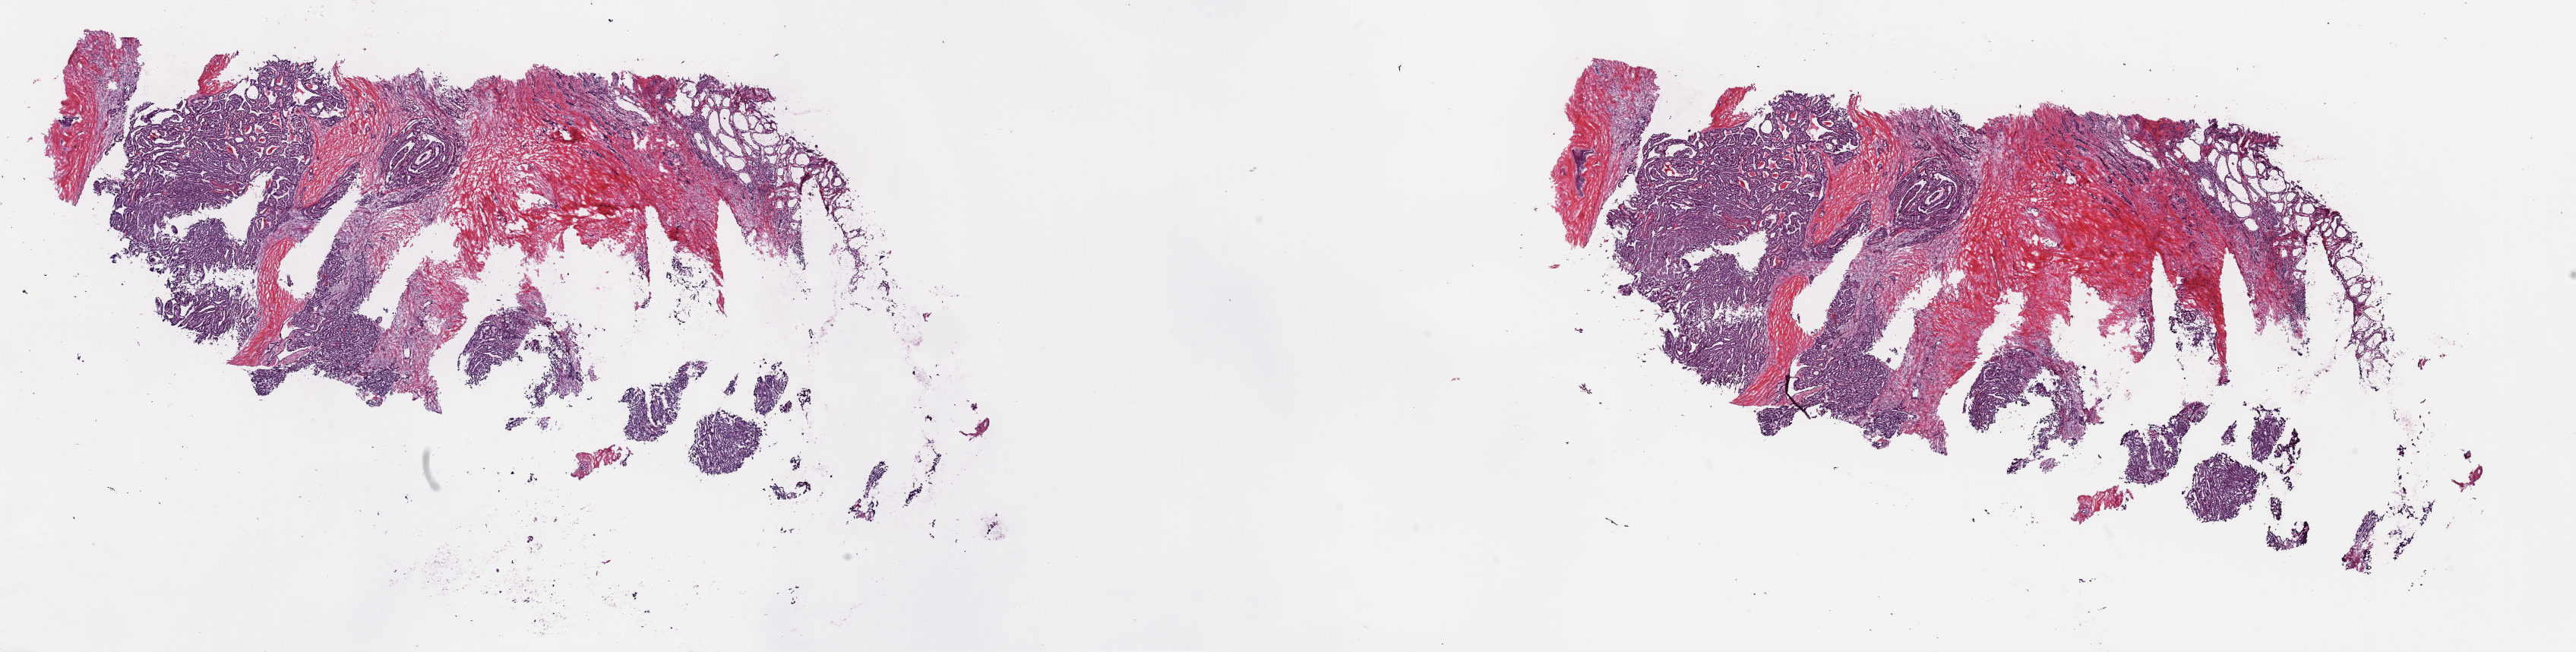
Whole-slide histology image, H&E-stained, shown as a low-resolution overview of the whole scanned area (about 26.8 x 6.8 mm, acquisition: 40x scan). Frozen section from the top of the tissue portion. Sample: primary tumour, thyroid. Female, age 40 years at initial diagnosis. Slide review estimates, as recorded: tumour cells 65%, tumour nuclei 70%.
Histologic diagnosis: Papillary adenocarcinoma, NOS (thyroid gland).